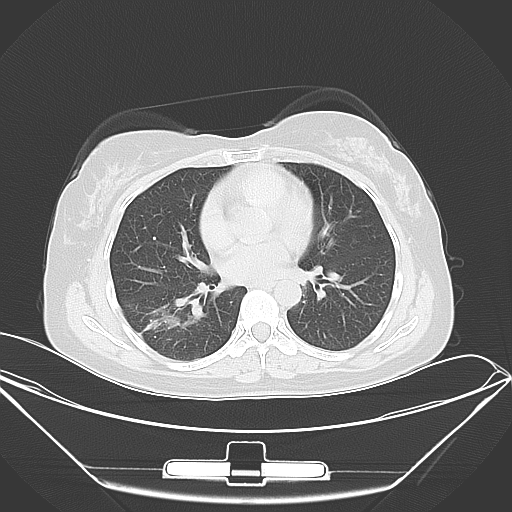
Chest CT, one axial slice. Position 19 of 46 along the scan axis. Lung window (W 1500 / L -600 HU). 5 mm slice thickness. 512 × 512 image matrix, field of view 407 × 407 mm. Patient: female, 42 years. From the clinical record (not read from this slice): clinical TNM (as recorded): T1c N0 M1a.
Annotated regions visible in this slice (rectangle marked by the reading radiologist):
- lung tumour (recorded histology: adenocarcinoma): bounding box <136,300,193,341> (left, top, right, bottom; pixels)